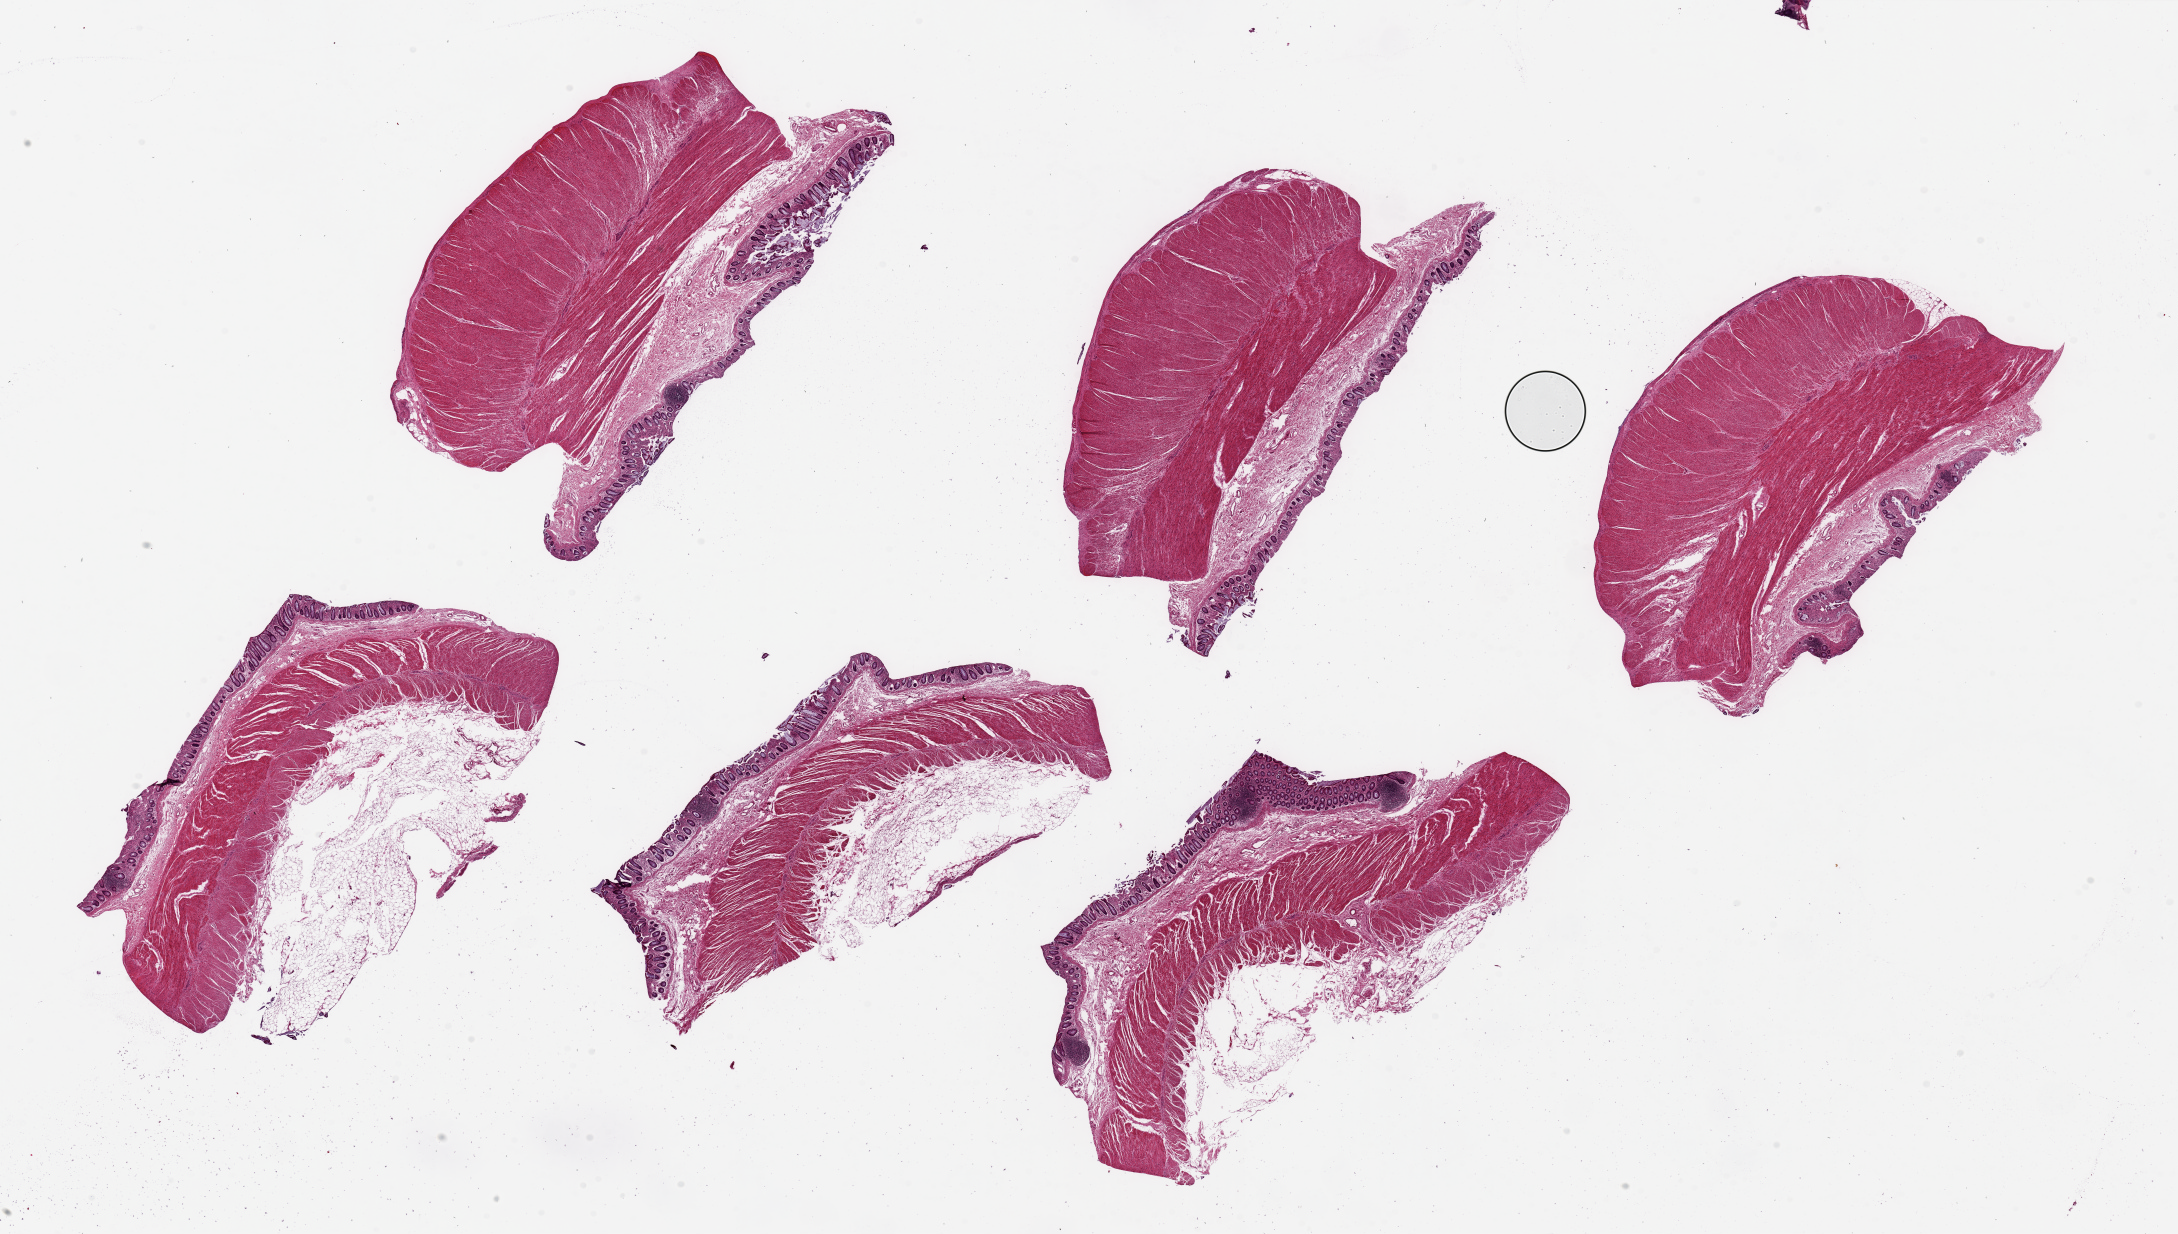
Whole-slide image, H&E stain, a low-resolution overview of the entire scanned area, about 34.5 x 19.5 mm. PAXgene-fixed paraffin-embedded (PFPE) section. Section of sigmoid colon (target tissue). Tissue donor sample. Donor: female.
Review note (as recorded): 6 pieces, up to 9x5mm; all are full thickness with up to 2 mm adipose, should only contain muscle without extramural adipose; muscle slightly autolyzed, mucosa moderately autolyzed.